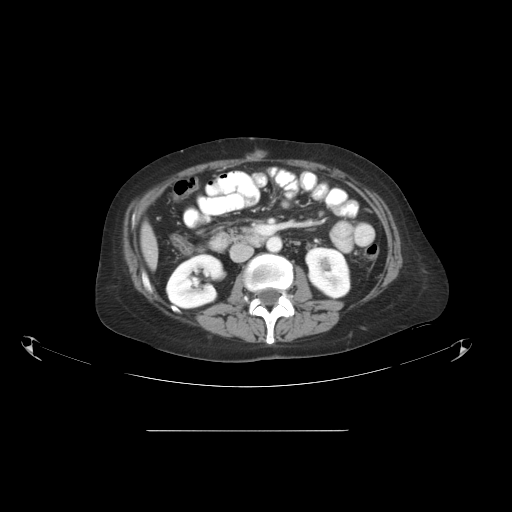
Contrast-enhanced abdominal CT, one axial slice; position 20 of 51 along the scan axis; intravenous contrast given; soft-tissue window (W 400 / L 40 HU); 5 mm slice thickness; 512 × 512 image matrix, field of view 475 × 475 mm. Female patient, age 48 years. From the clinical record (not read from this slice): diagnosis: colorectal cancer liver metastases, imaged before liver resection; multiple liver metastases: yes; largest metastasis: 1 cm; disease in both lobes: no.
Outlined on this slice (expert manual segmentation):
- liver: box from (x=141, y=225) to (x=158, y=267) px
- planned liver remnant (the part of the liver to remain after resection): (x=141, y=225)–(x=158, y=267)